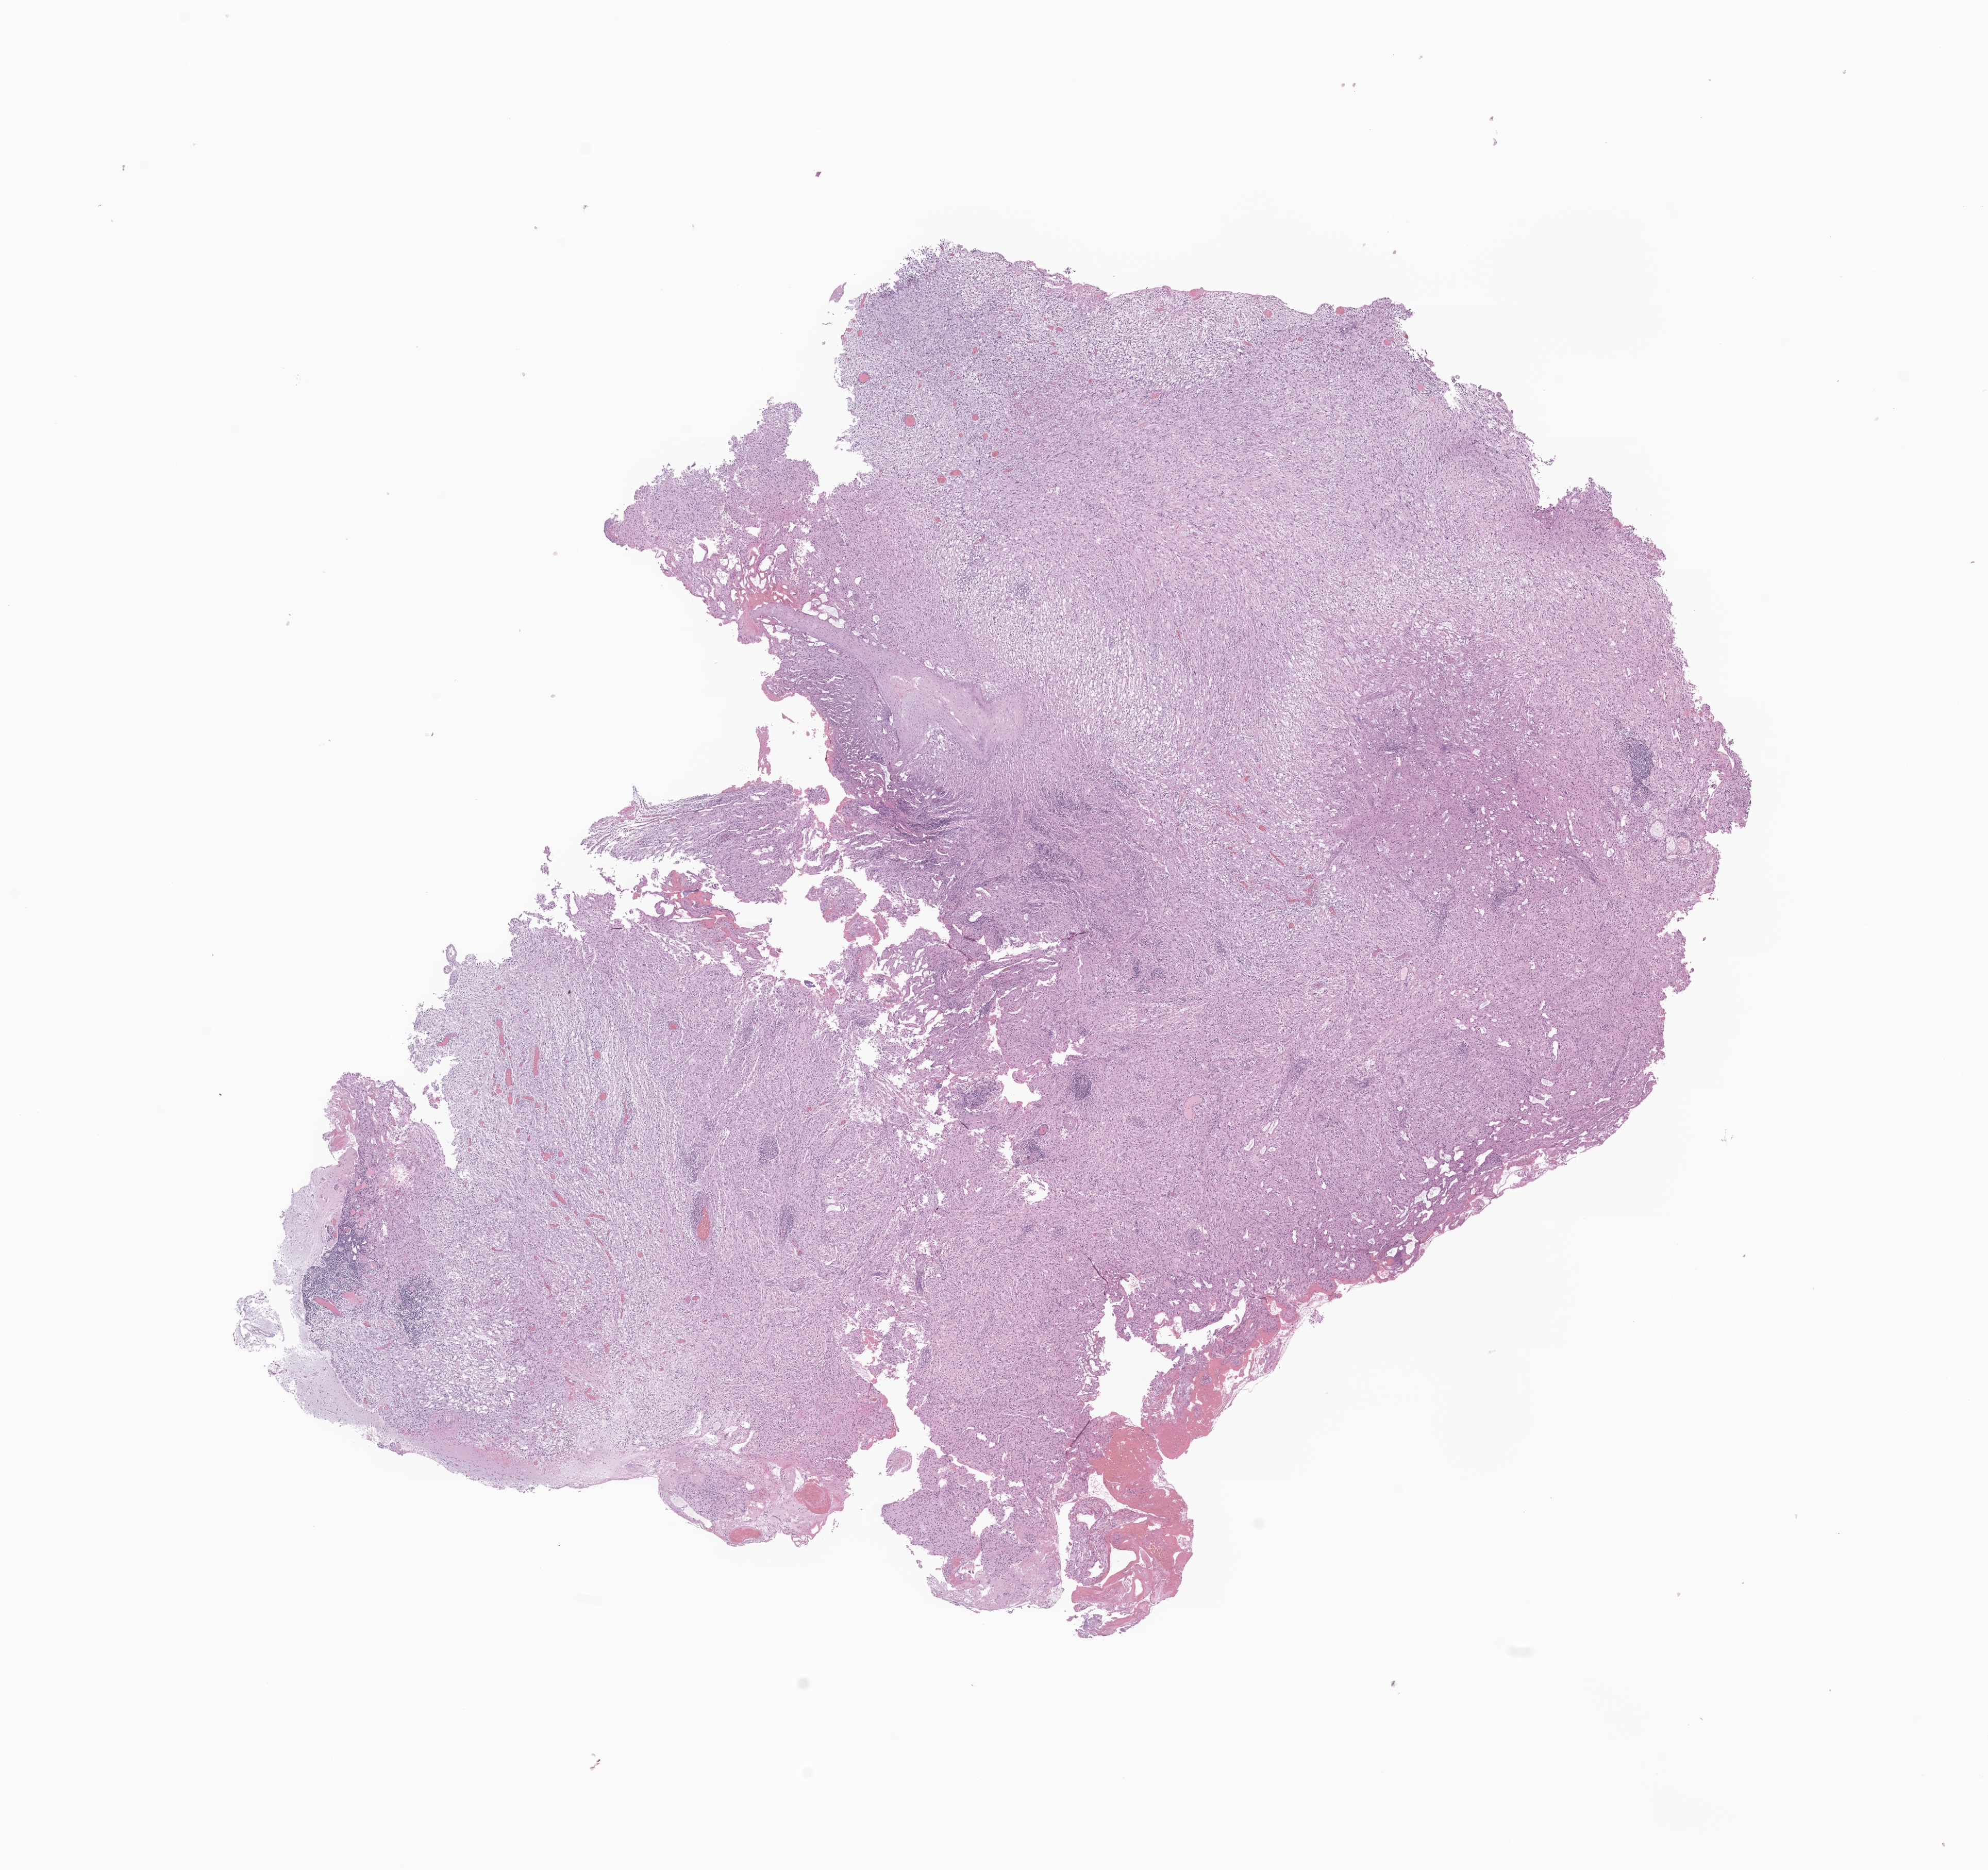
Digitized H&E-stained section of tumor tissue from the brain — whole scanned area (about 16.3 x 15.3 mm) shown as a low-resolution overview; formalin-fixed paraffin-embedded section. Patient: male, age 174 months (14 years 6 months).
Recorded diagnosis: Pleomorphic xanthoastrocytoma, NOS.